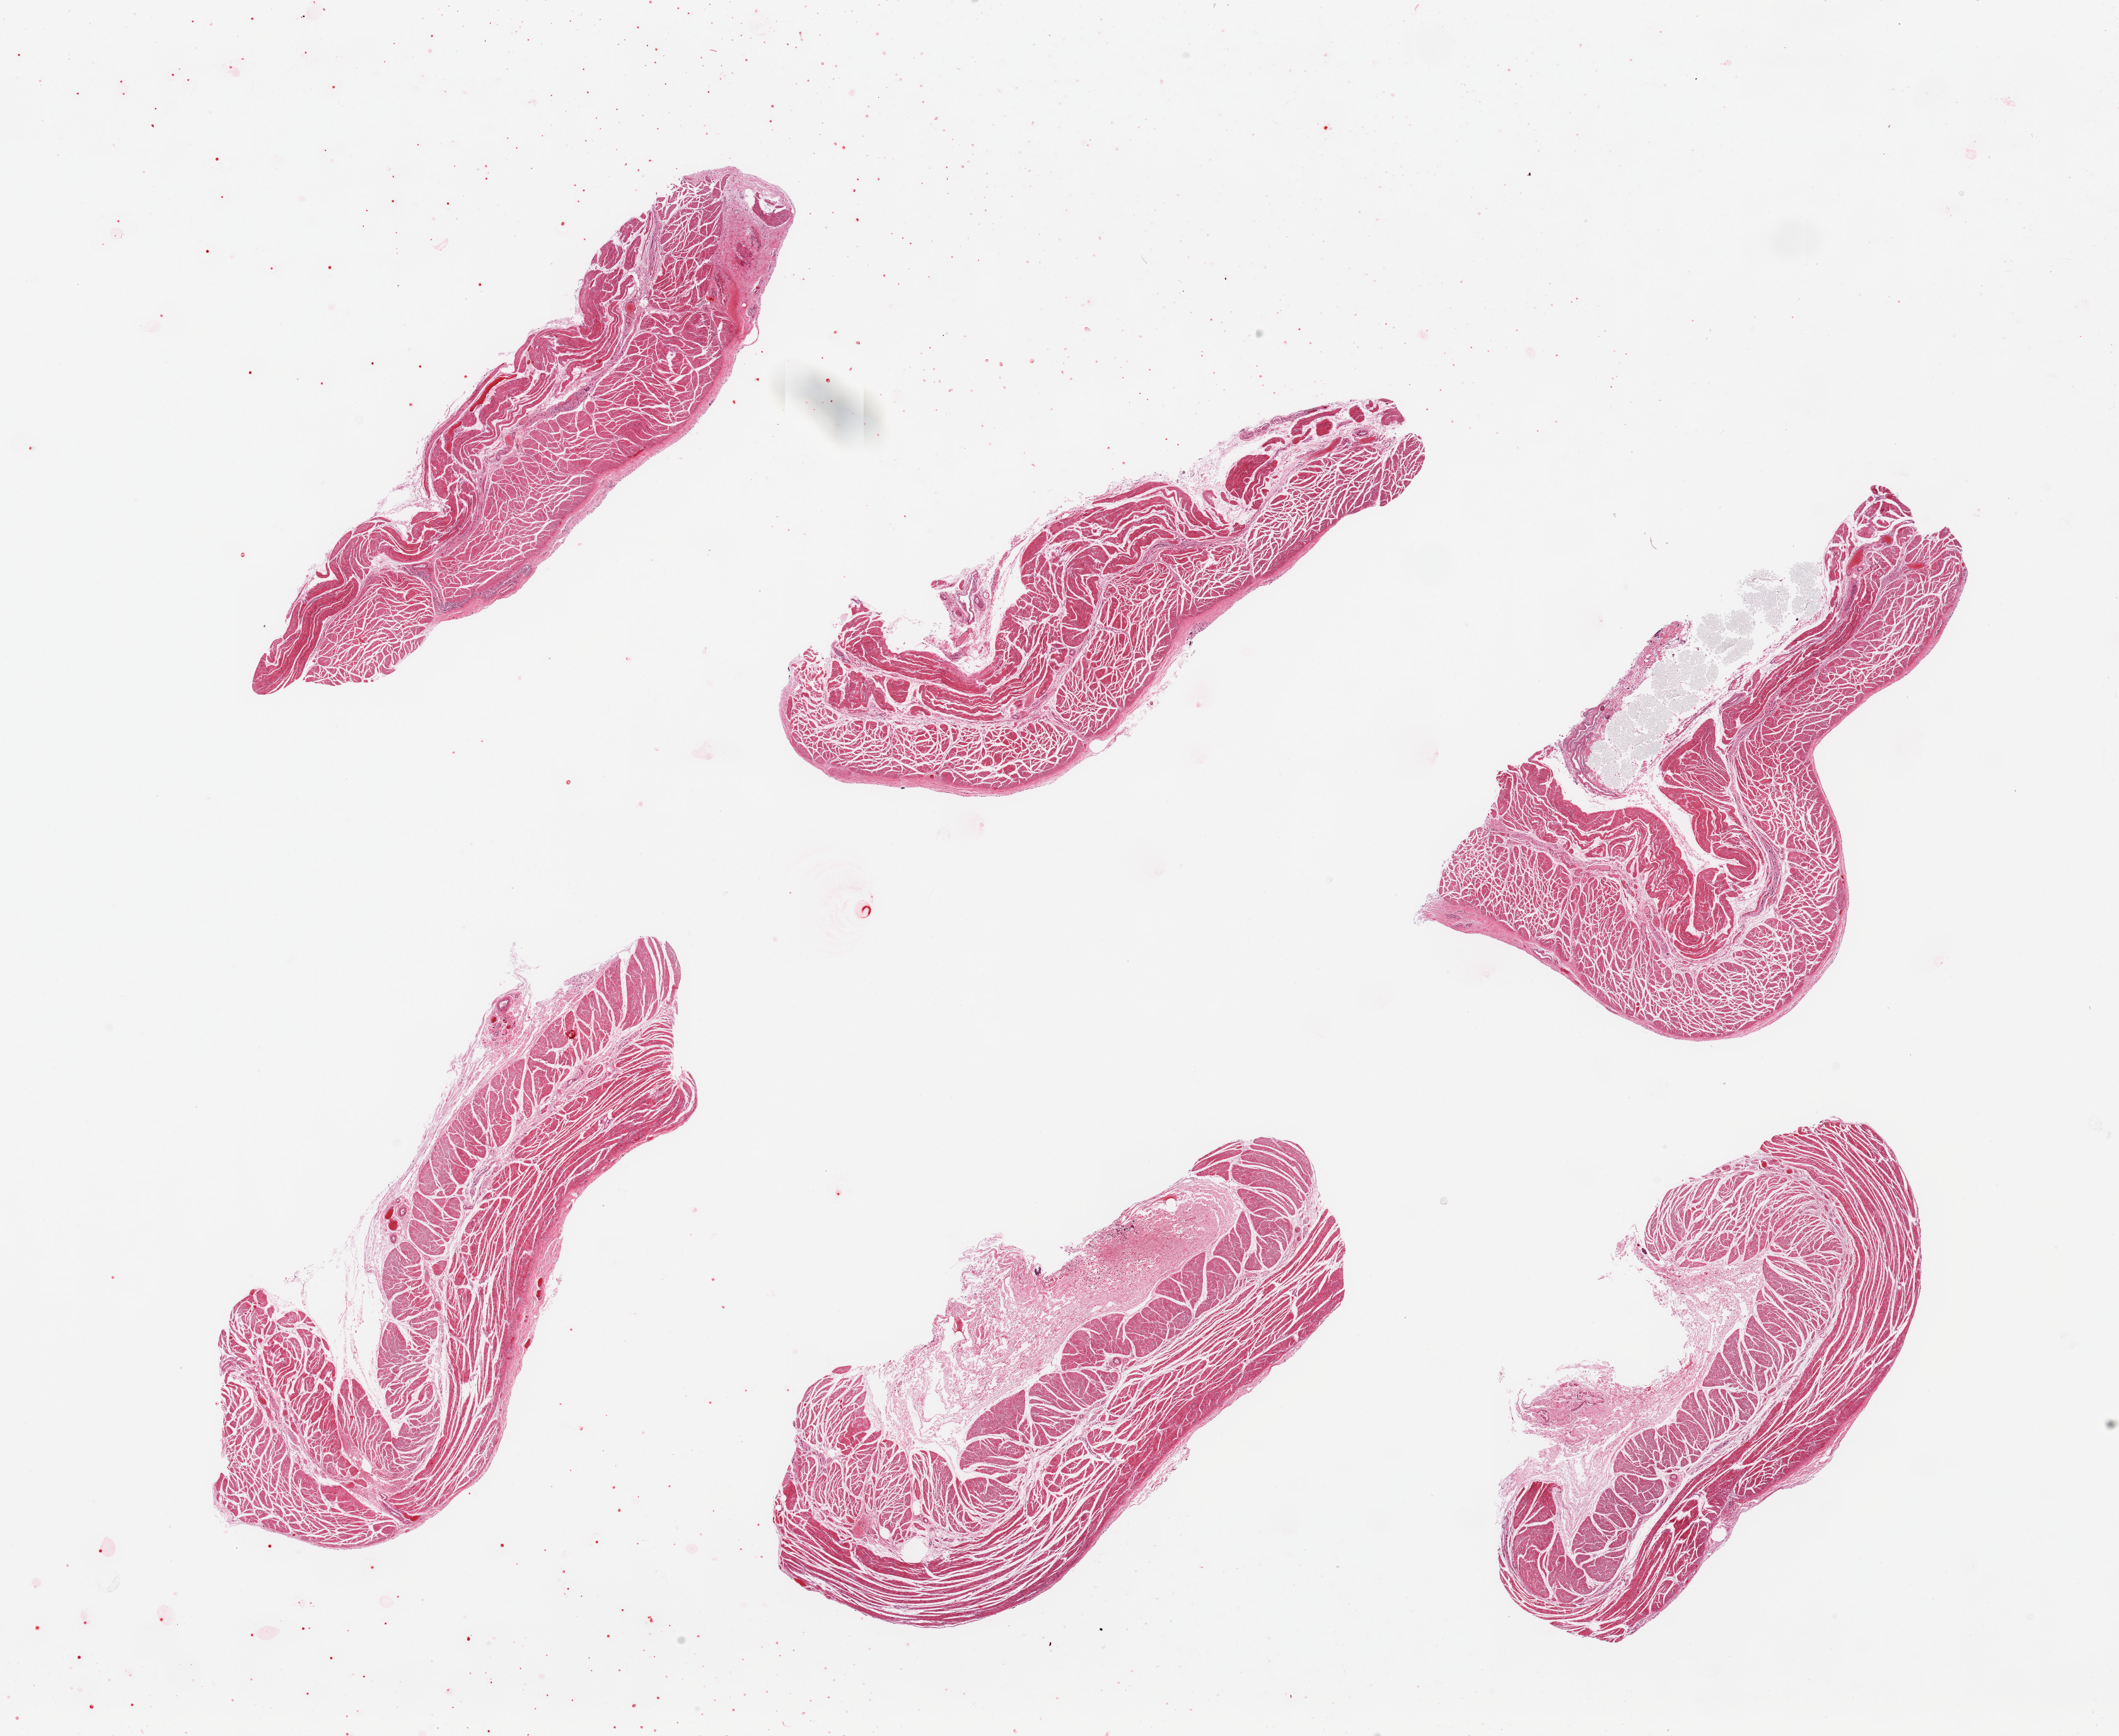
Digitized H&E-stained section, whole scanned area (about 26.6 x 21.8 mm) shown as a low-resolution overview, PAXgene-fixed paraffin-embedded (PFPE) section, target tissue: esophageal muscle, tissue donor sample. Female donor.
Pathologist's review note for this sample: 6 pieces, confirmed target muscularis.